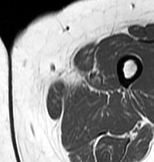
MRI of an extremity soft-tissue mass, one axial slice. Position 1 of 83 along the scan axis. MR volume resampled by the dataset authors to the PET/CT grid (not the native acquisition matrix). 154 × 162 image matrix, field of view 150 × 158 mm. Female patient. Case-level facts recorded for this patient, not image findings: histological type: myxofibrosarcoma; grade: intermediate; site of the primary tumour: left thigh.
Annotated regions visible in this slice (expert contour drawn on MRI and transferred to this co-registered scan by the dataset authors):
- gross tumour volume including surrounding oedema: bounding box <55,75,104,94> (left, top, right, bottom; pixels)